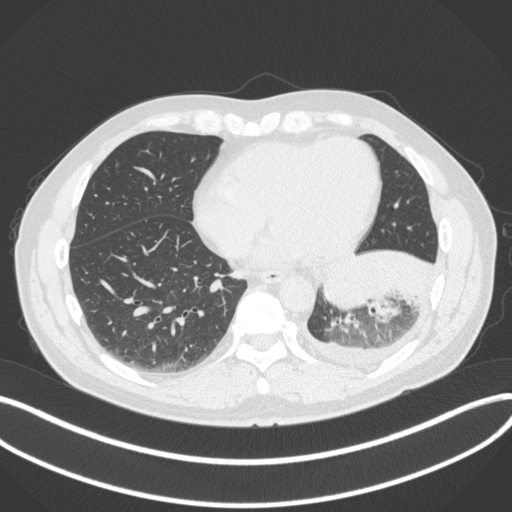
Chest CT, one axial slice; position 118 of 350 along the scan axis; reconstruction kernel B31f; 120 kVp; lung window (W 1500 / L -600 HU); 512 × 512 image matrix, field of view 400 × 400 mm. Male patient, age 58 years. From the clinical record (not read from this slice): clinical TNM (as recorded): T3 N1 M1b.
Annotated regions visible in this slice (rectangle marked by the reading radiologist):
- lung tumour (recorded histology: small cell carcinoma): box from (x=322, y=256) to (x=371, y=317) px